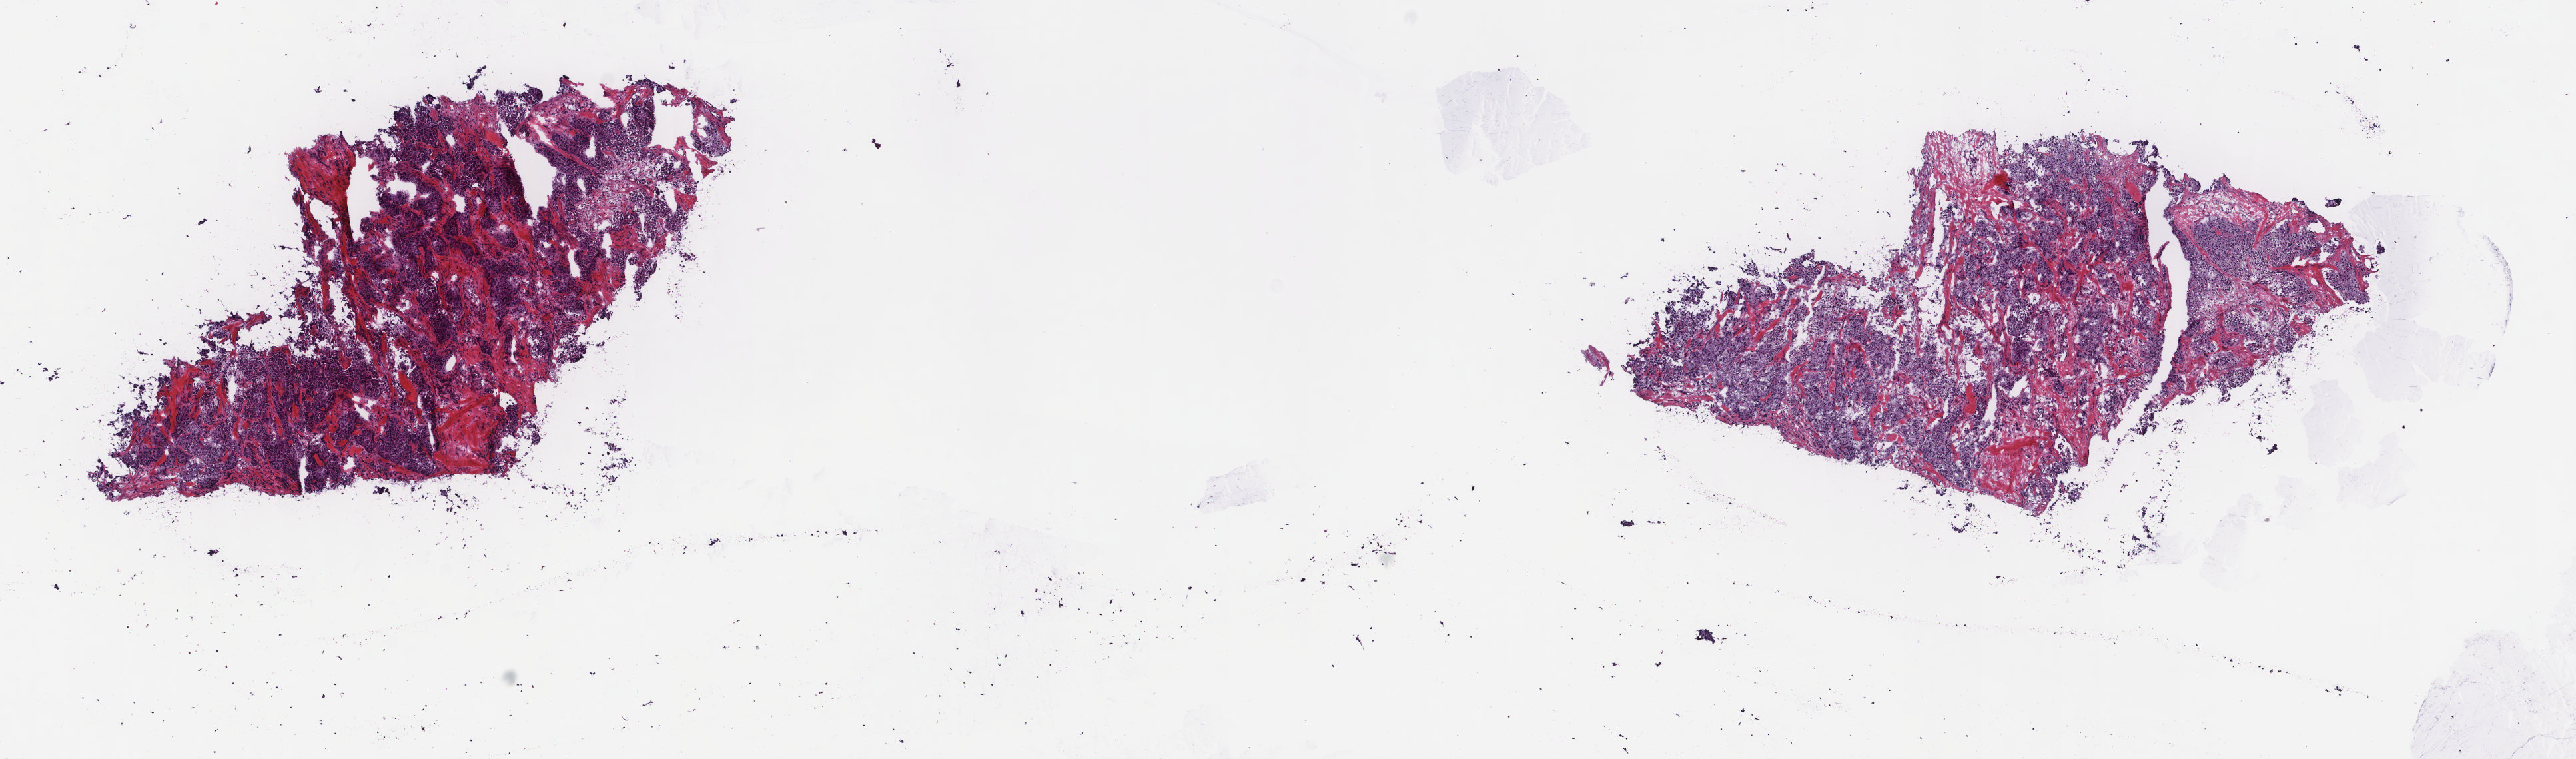
Whole-slide histology image, H&E, a low-resolution overview of the entire scanned area, about 15.3 x 4.5 mm, frozen section from the top of the tissue portion, primary tumour sample from the breast. Patient: female, age at initial diagnosis 68 years. Slide review estimates, as recorded: tumour cells 100%, tumour nuclei 90%, normal cells 0%, stromal cells 0%, necrosis 0%. Inflammatory infiltration, as recorded: lymphocyte infiltration 0%, monocyte infiltration 0%, neutrophil infiltration 0%.
AJCC pathologic stage: IIB (5th edition). Laterality: right. Diagnosis: Infiltrating duct carcinoma, NOS. TNM: T2 N1 M0.